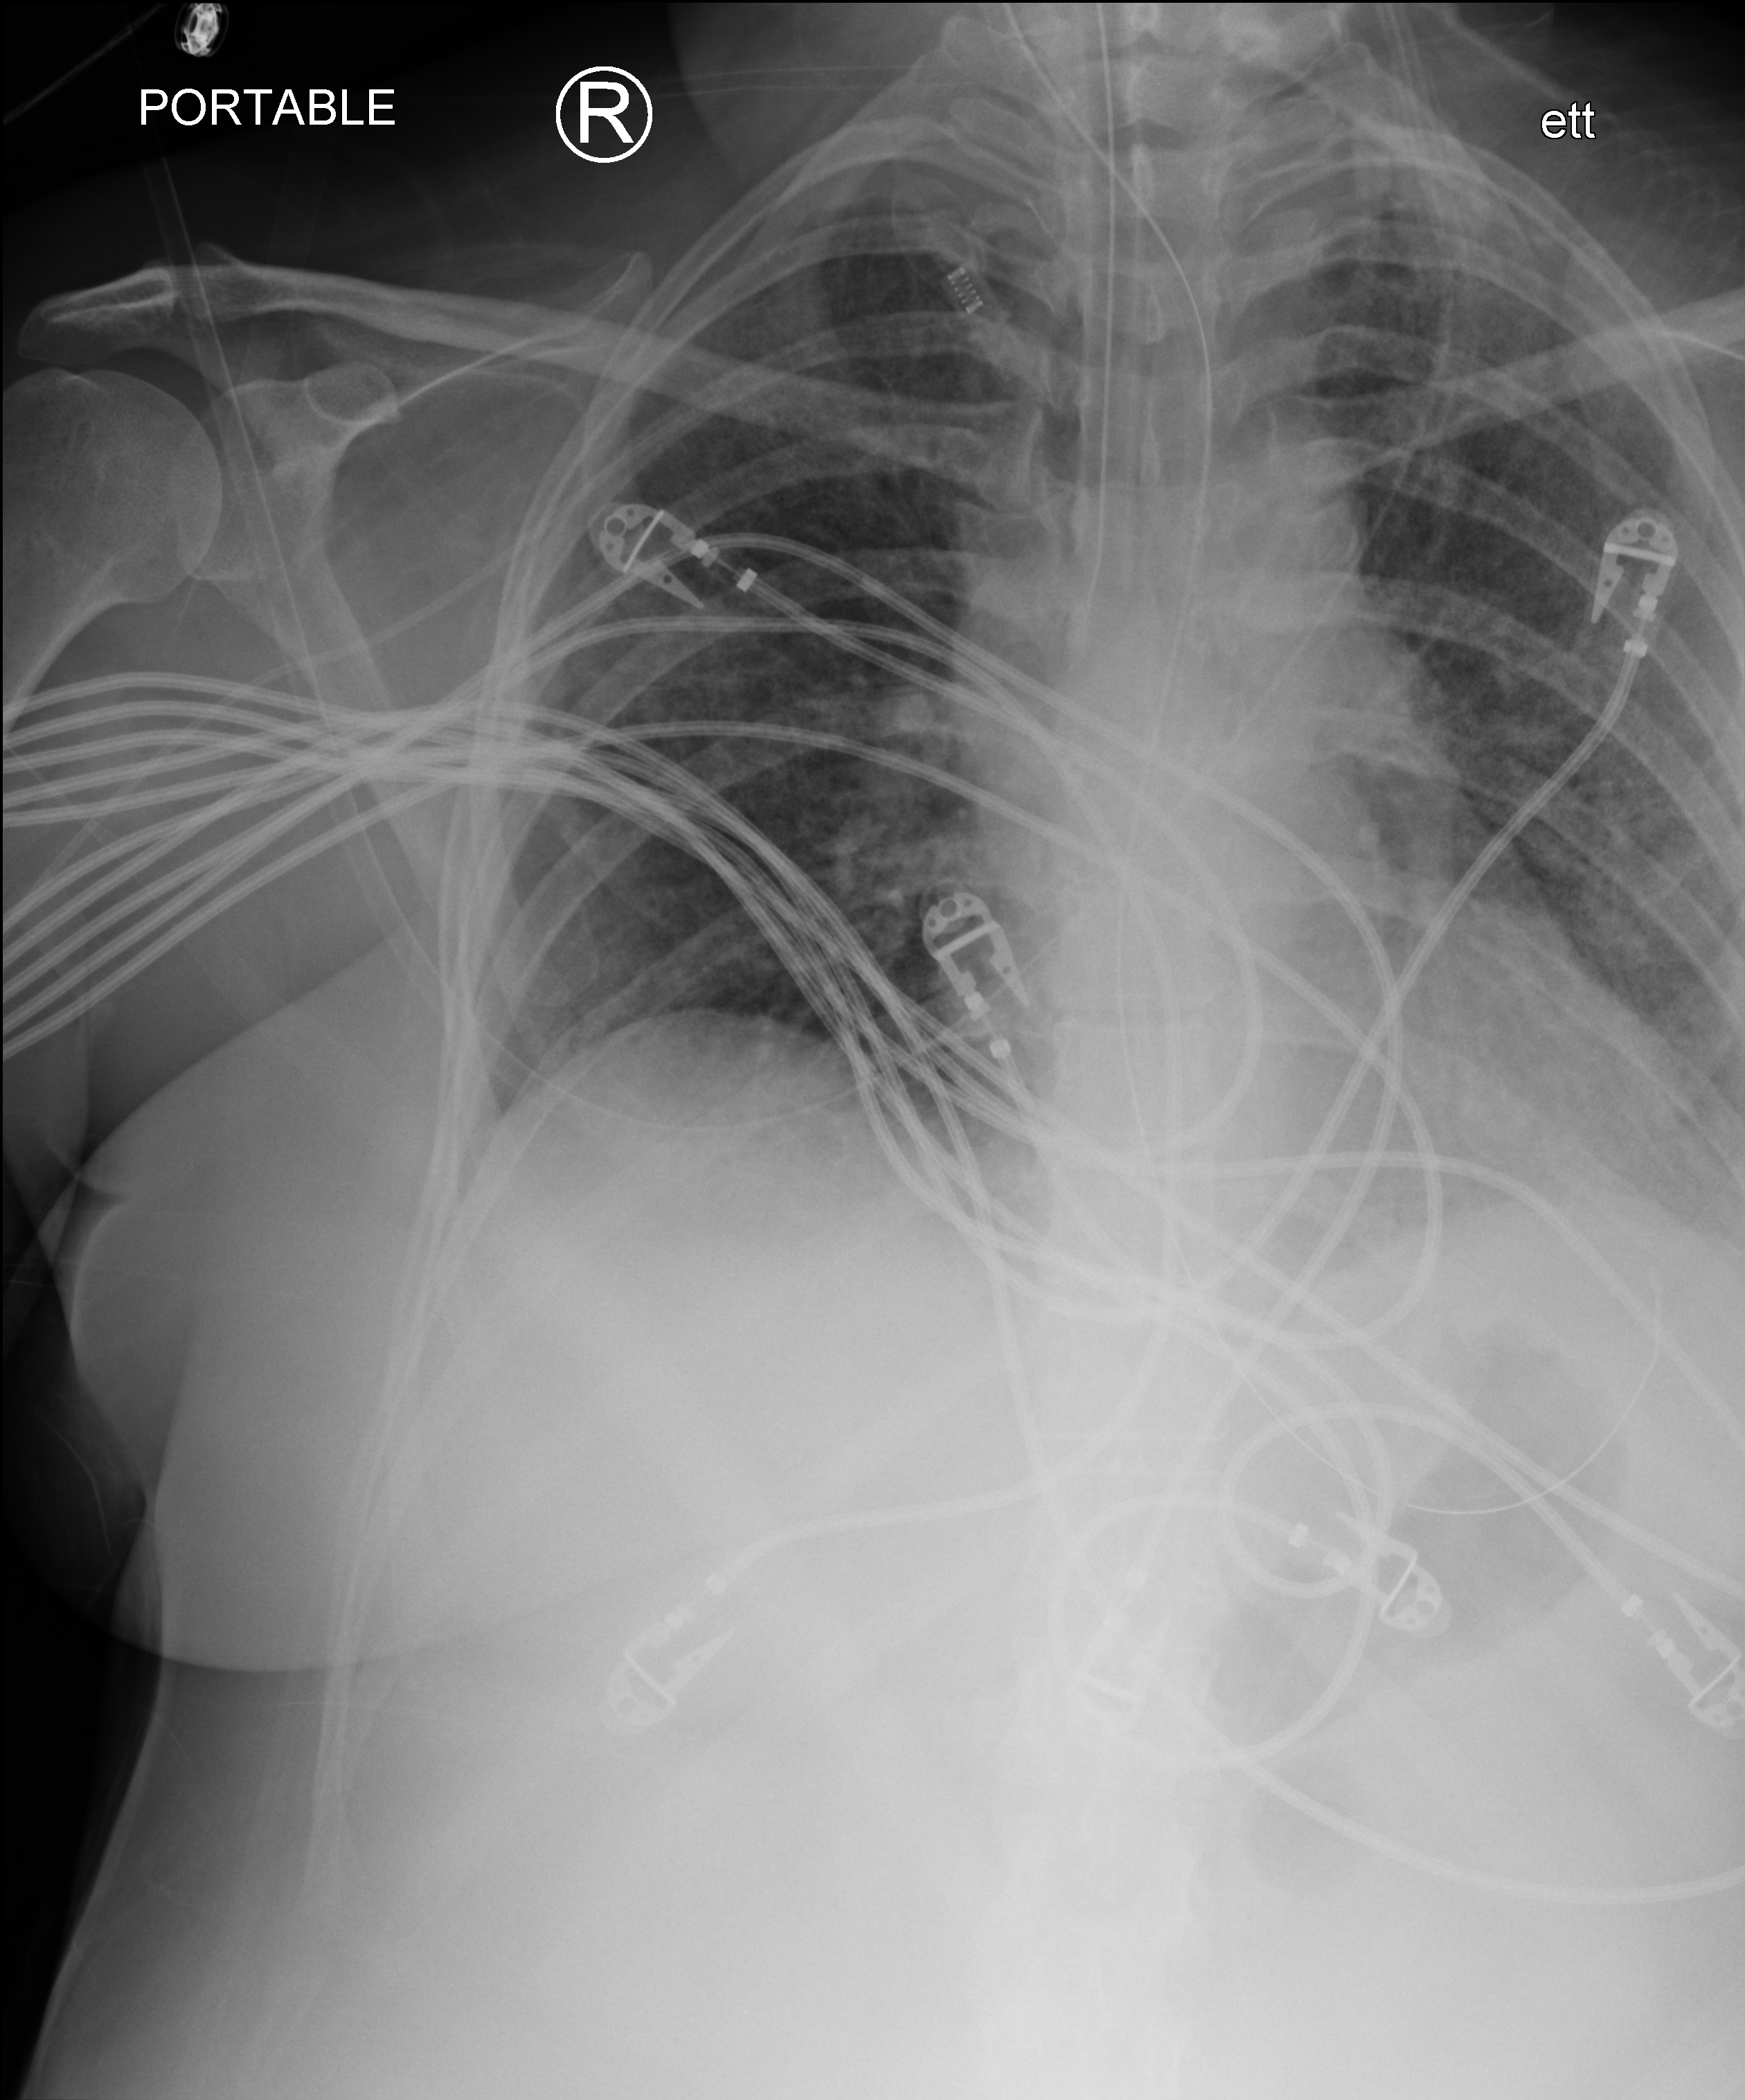
Chest X-ray (portable); anteroposterior (AP) projection. Female patient hospitalised with COVID-19, age 18–59 years.
From the hospital-stay record, not from the radiograph (when in the stay this image was taken is not recorded): mechanically ventilated during this hospital stay: yes; admitted to intensive care during this hospital stay: yes.